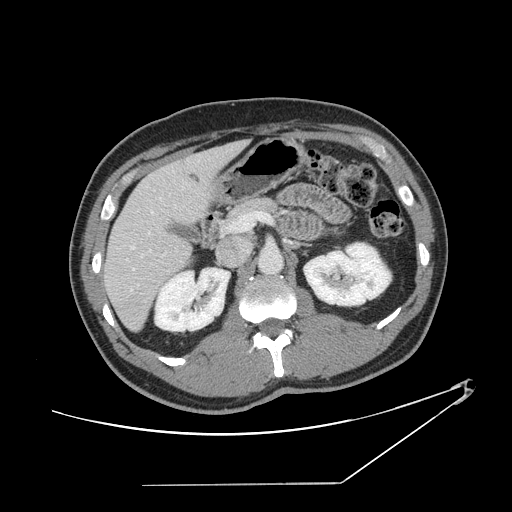
Contrast-enhanced abdominal CT, one axial slice; slice 73 of 152 in the series (ordered by position); reconstruction kernel STANDARD; 120 kVp; intravenous contrast given; soft-tissue window (W 400 / L 40 HU); 512 × 512 image matrix, field of view 432 × 432 mm. Male patient, age 45 years. Case-level facts recorded for this patient, not image findings: diagnosis: colorectal cancer liver metastases, imaged before liver resection; multiple liver metastases: no; largest metastasis: 1 cm; disease in both lobes: no.
Structures marked on this image (expert manual segmentation):
- hepatic veins: box from (x=129, y=161) to (x=199, y=291) px
- liver: (x=105, y=142)–(x=245, y=330)
- planned liver remnant (the part of the liver to remain after resection): (x=105, y=159)–(x=207, y=330)
- portal vein (with intrahepatic branches): (x=133, y=212)–(x=272, y=270)